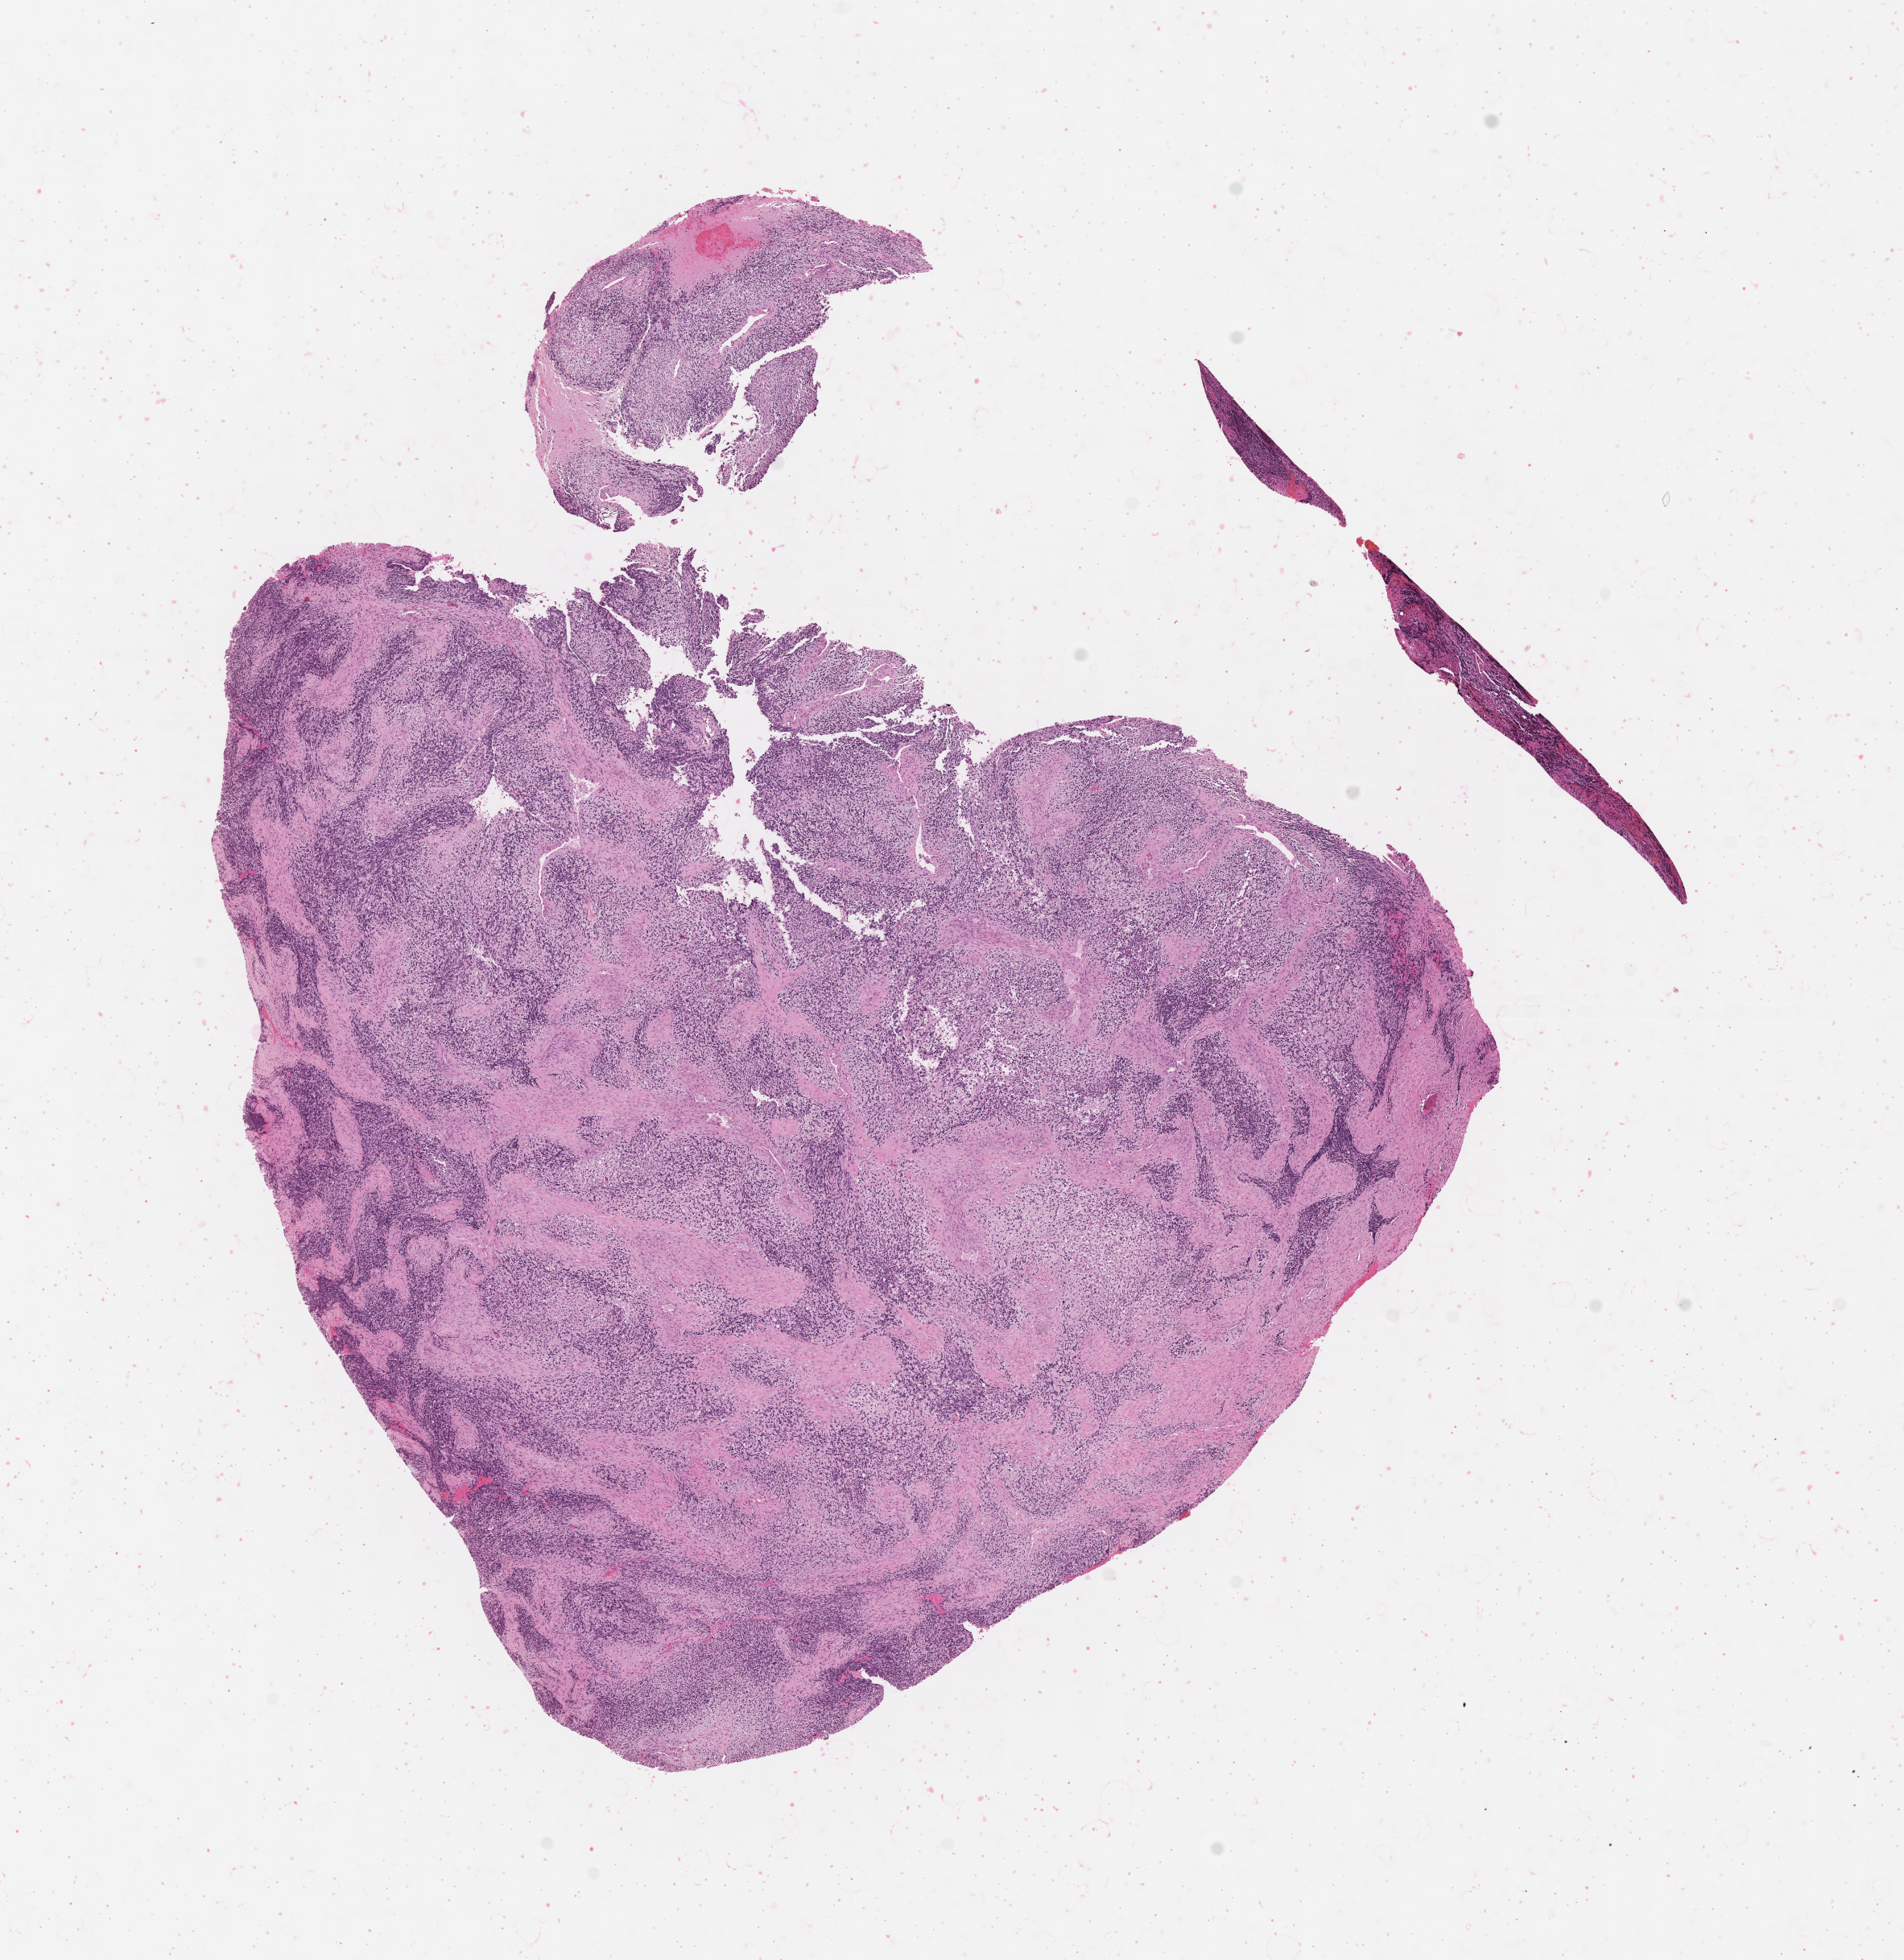
Whole-slide image, hematoxylin and eosin (H&E) stain of tumor tissue — shown as a low-resolution overview of the whole scanned area (about 9.6 x 9.8 mm). Formalin-fixed paraffin-embedded section. Site: mandible, right. Male patient, age at diagnosis 5.5 years.
* diagnosis: rhabdomyosarcoma; histological classification: embryonal rhabdomyosarcoma
* stage (as recorded): 1